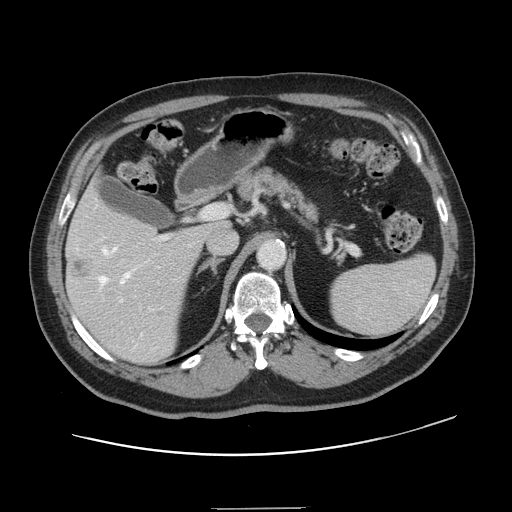
Contrast-enhanced abdominal CT, one axial slice; soft-tissue window (W 400 / L 40 HU); 512 × 512 image matrix, field of view 402 × 402 mm. Male patient, age 62 years. Case-level facts recorded for this patient, not image findings: diagnosis: colorectal cancer liver metastases, imaged before liver resection; multiple liver metastases: yes; largest metastasis: 2.7 cm; disease in both lobes: no.
Structures marked on this image (expert manual segmentation):
- hepatic veins: bounding box [x1, y1, x2, y2] px = [100, 248, 142, 335]
- liver: [67, 186, 219, 363]
- planned liver remnant (the part of the liver to remain after resection): [69, 187, 219, 242]
- portal vein (with intrahepatic branches): [120, 206, 220, 302]
- liver metastasis: [70, 257, 91, 280]